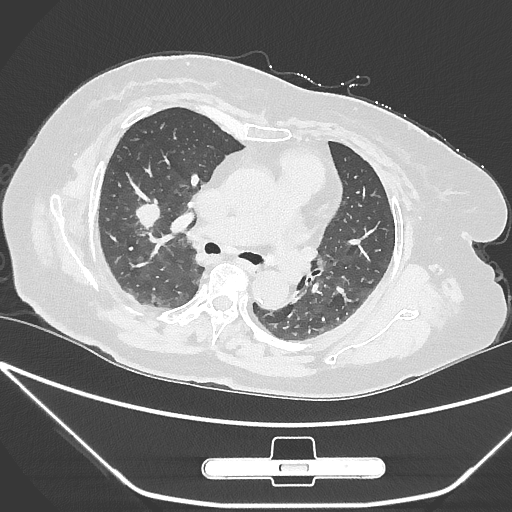
Chest CT, one axial slice. Reconstruction kernel IMR1,SharpPlus. Lung window (W 1500 / L -600 HU). 1 mm slice thickness. 512 × 512 image matrix. Patient: female, 65 years. Case-level facts recorded for this patient, not image findings: clinical TNM (as recorded): T1c N0 M0; histopathological grade: G3.
Structures marked on this image (bounding box drawn by a radiologist):
- lung tumour (recorded histology: adenocarcinoma): bounding box (x1, y1, x2, y2) in pixels: (131, 193, 172, 239)